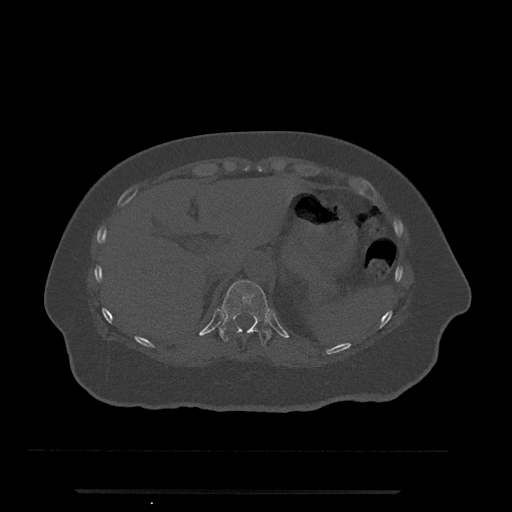
CT including the spine, one axial slice; position 239 of 797 along the scan axis; reconstruction kernel Br40s/3; bone window (W 1800 / L 400 HU); 0.5 mm slice thickness; 512 × 512 image matrix, field of view 440 × 440 mm. Patient: female, 51 years. From the clinical record (not read from this slice): primary cancer: neuro; vertebrae with lytic lesions (as recorded): T8.
Annotated regions visible in this slice (semi-automatically segmented with operator editing):
- T11 vertebra: box from (x=219, y=280) to (x=271, y=346) px